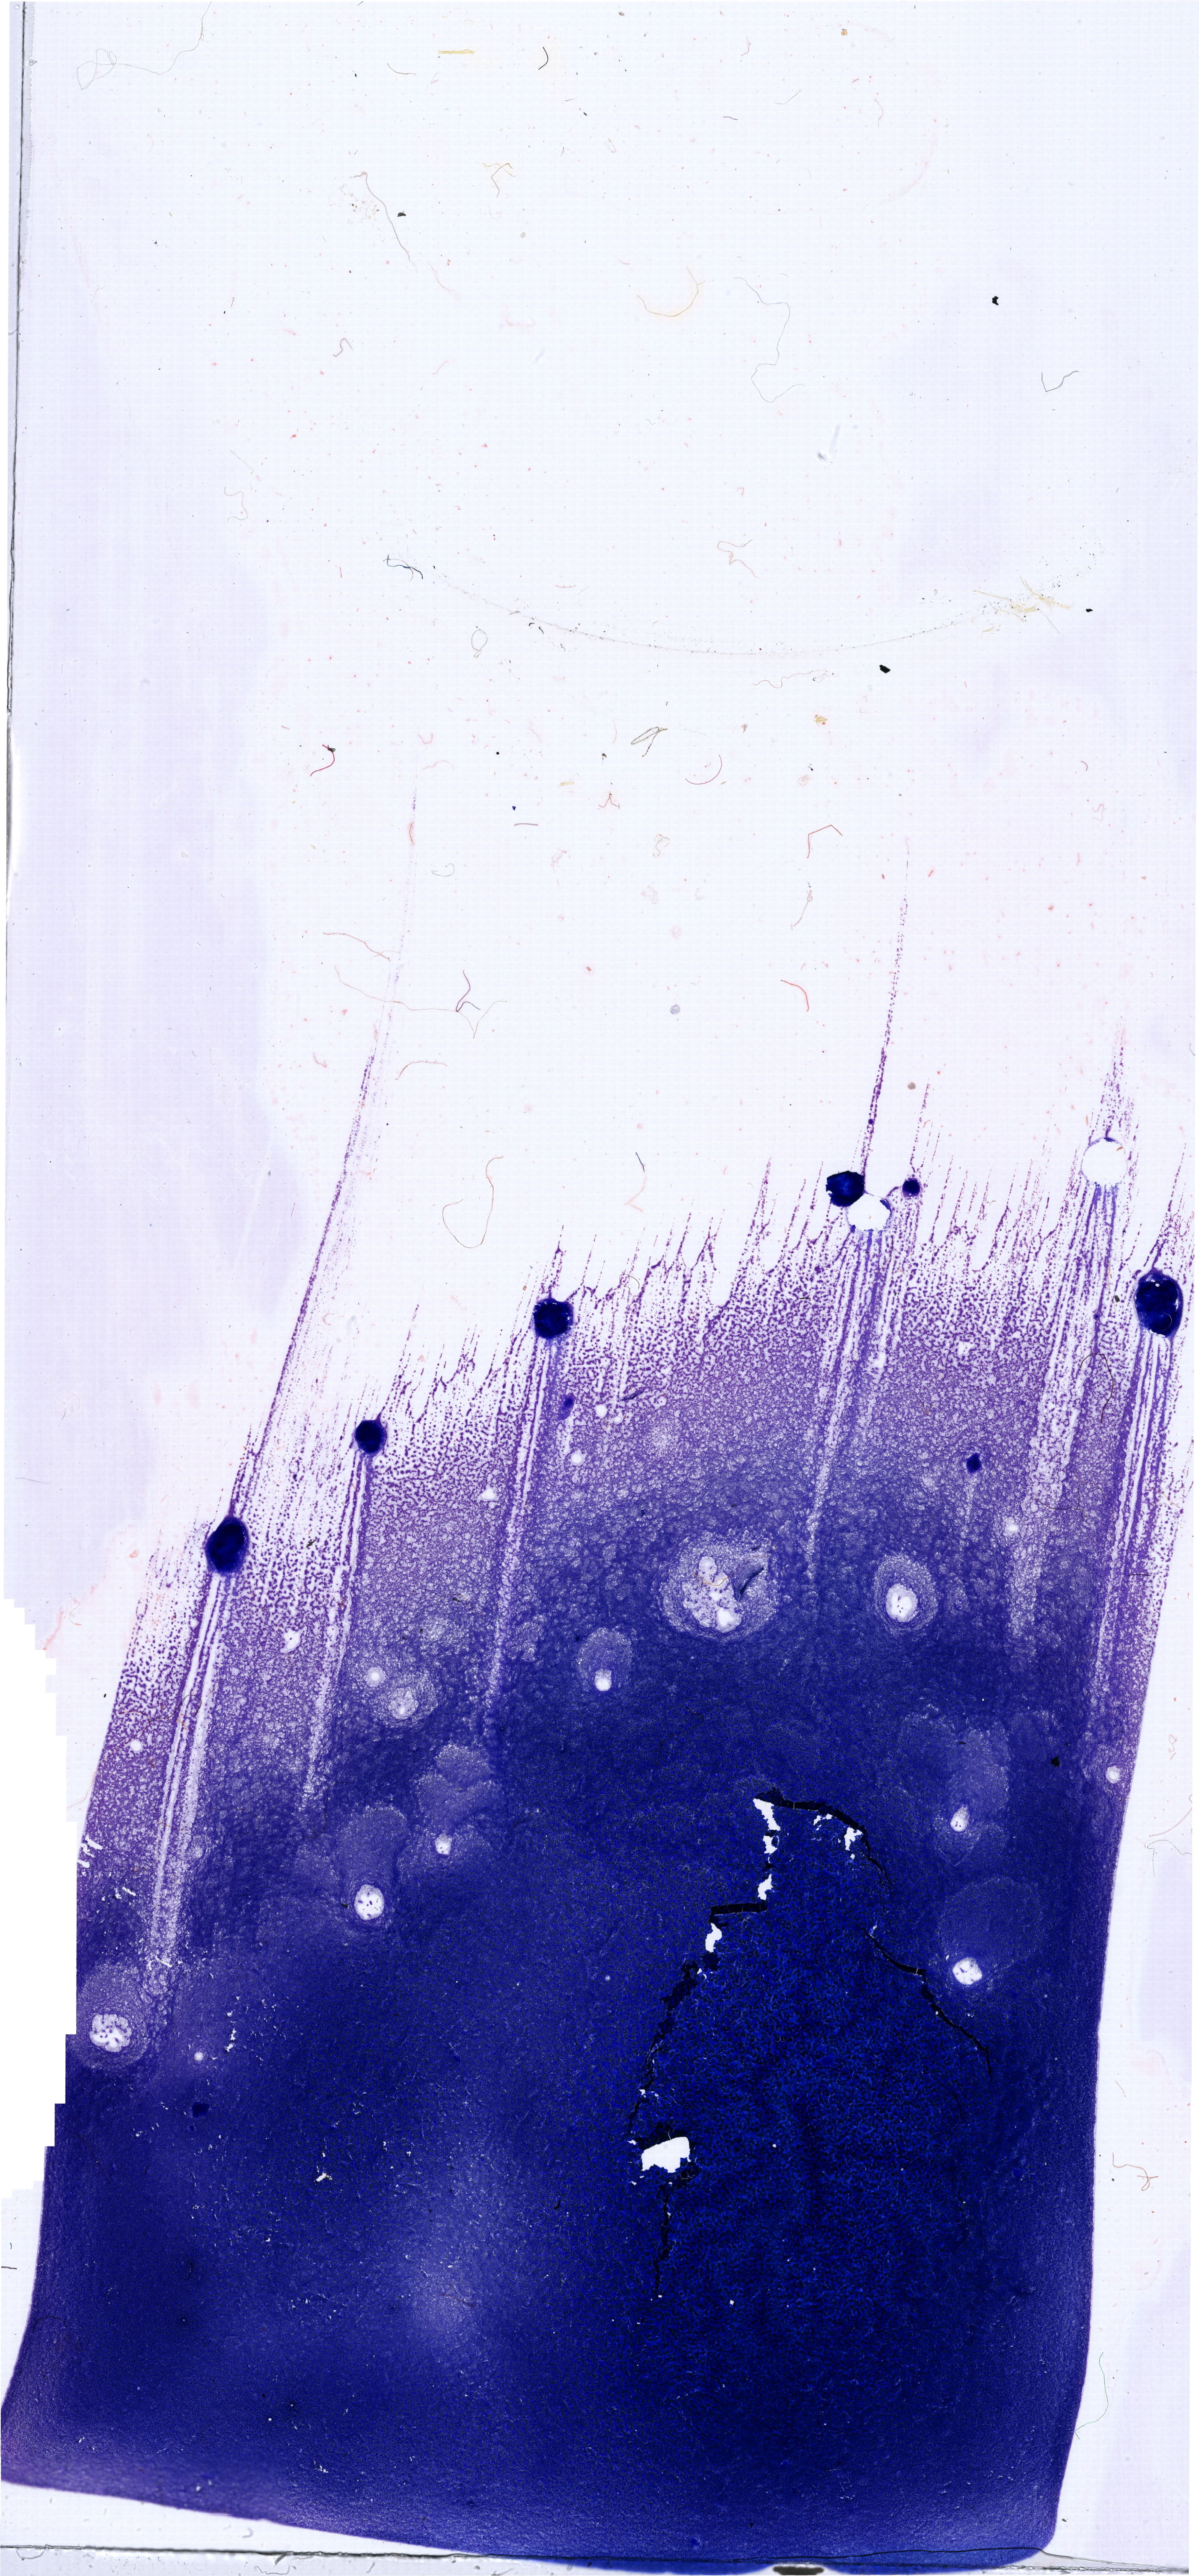
Bone marrow aspirate smear, May-Grünwald-Giemsa (MGG) stain, whole-slide image, a low-resolution overview of the entire scanned area, about 21.9 x 47.0 mm. Patient sex: female.
• diagnosis: Mixed Phenotype Acute Leukemia, B/Myeloid